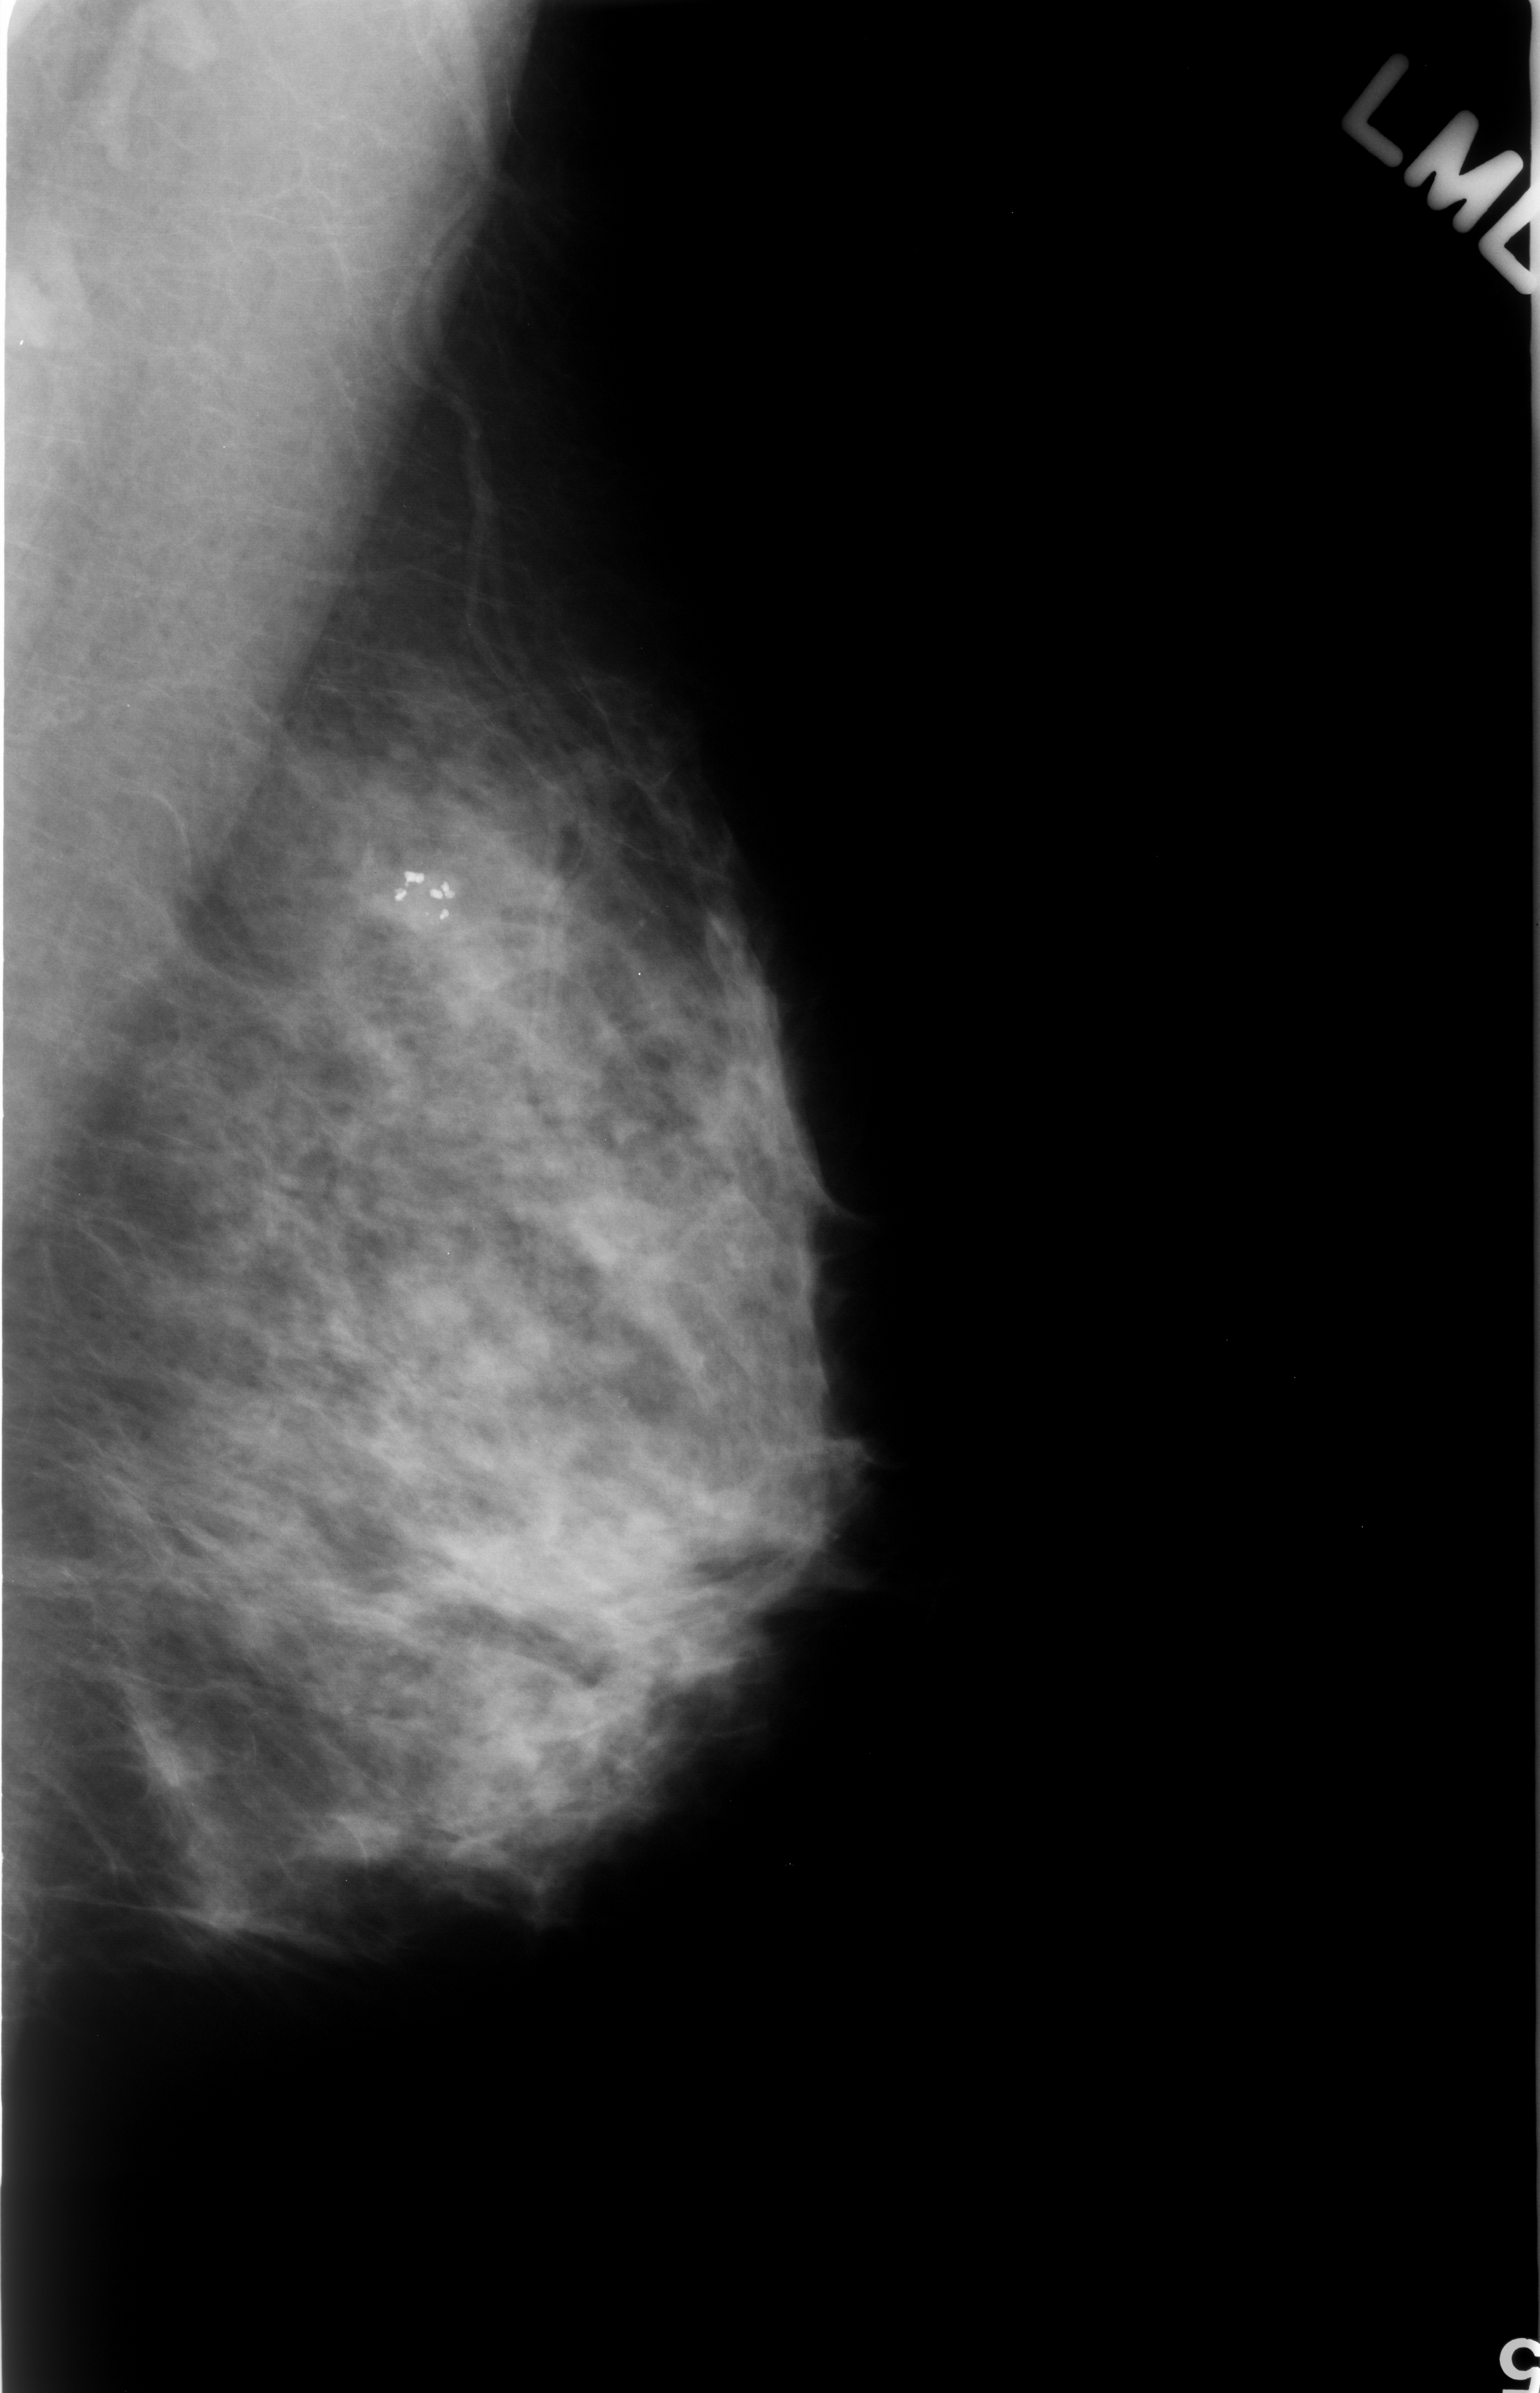
Mammogram (digitized film). Left breast. MLO view. Breast composition: heterogeneously dense (BI-RADS density category 3 of 4). 1540 × 2393 image matrix.
Marked abnormalities (boxes around the expert regions of interest):
- calcifications, morphology dystrophic, distribution clustered; BI-RADS assessment category 2; benign; no additional work-up was recommended (outcome (as recorded, no biopsy): benign without callback): bounding box [x1, y1, x2, y2] px = [354, 822, 469, 942]